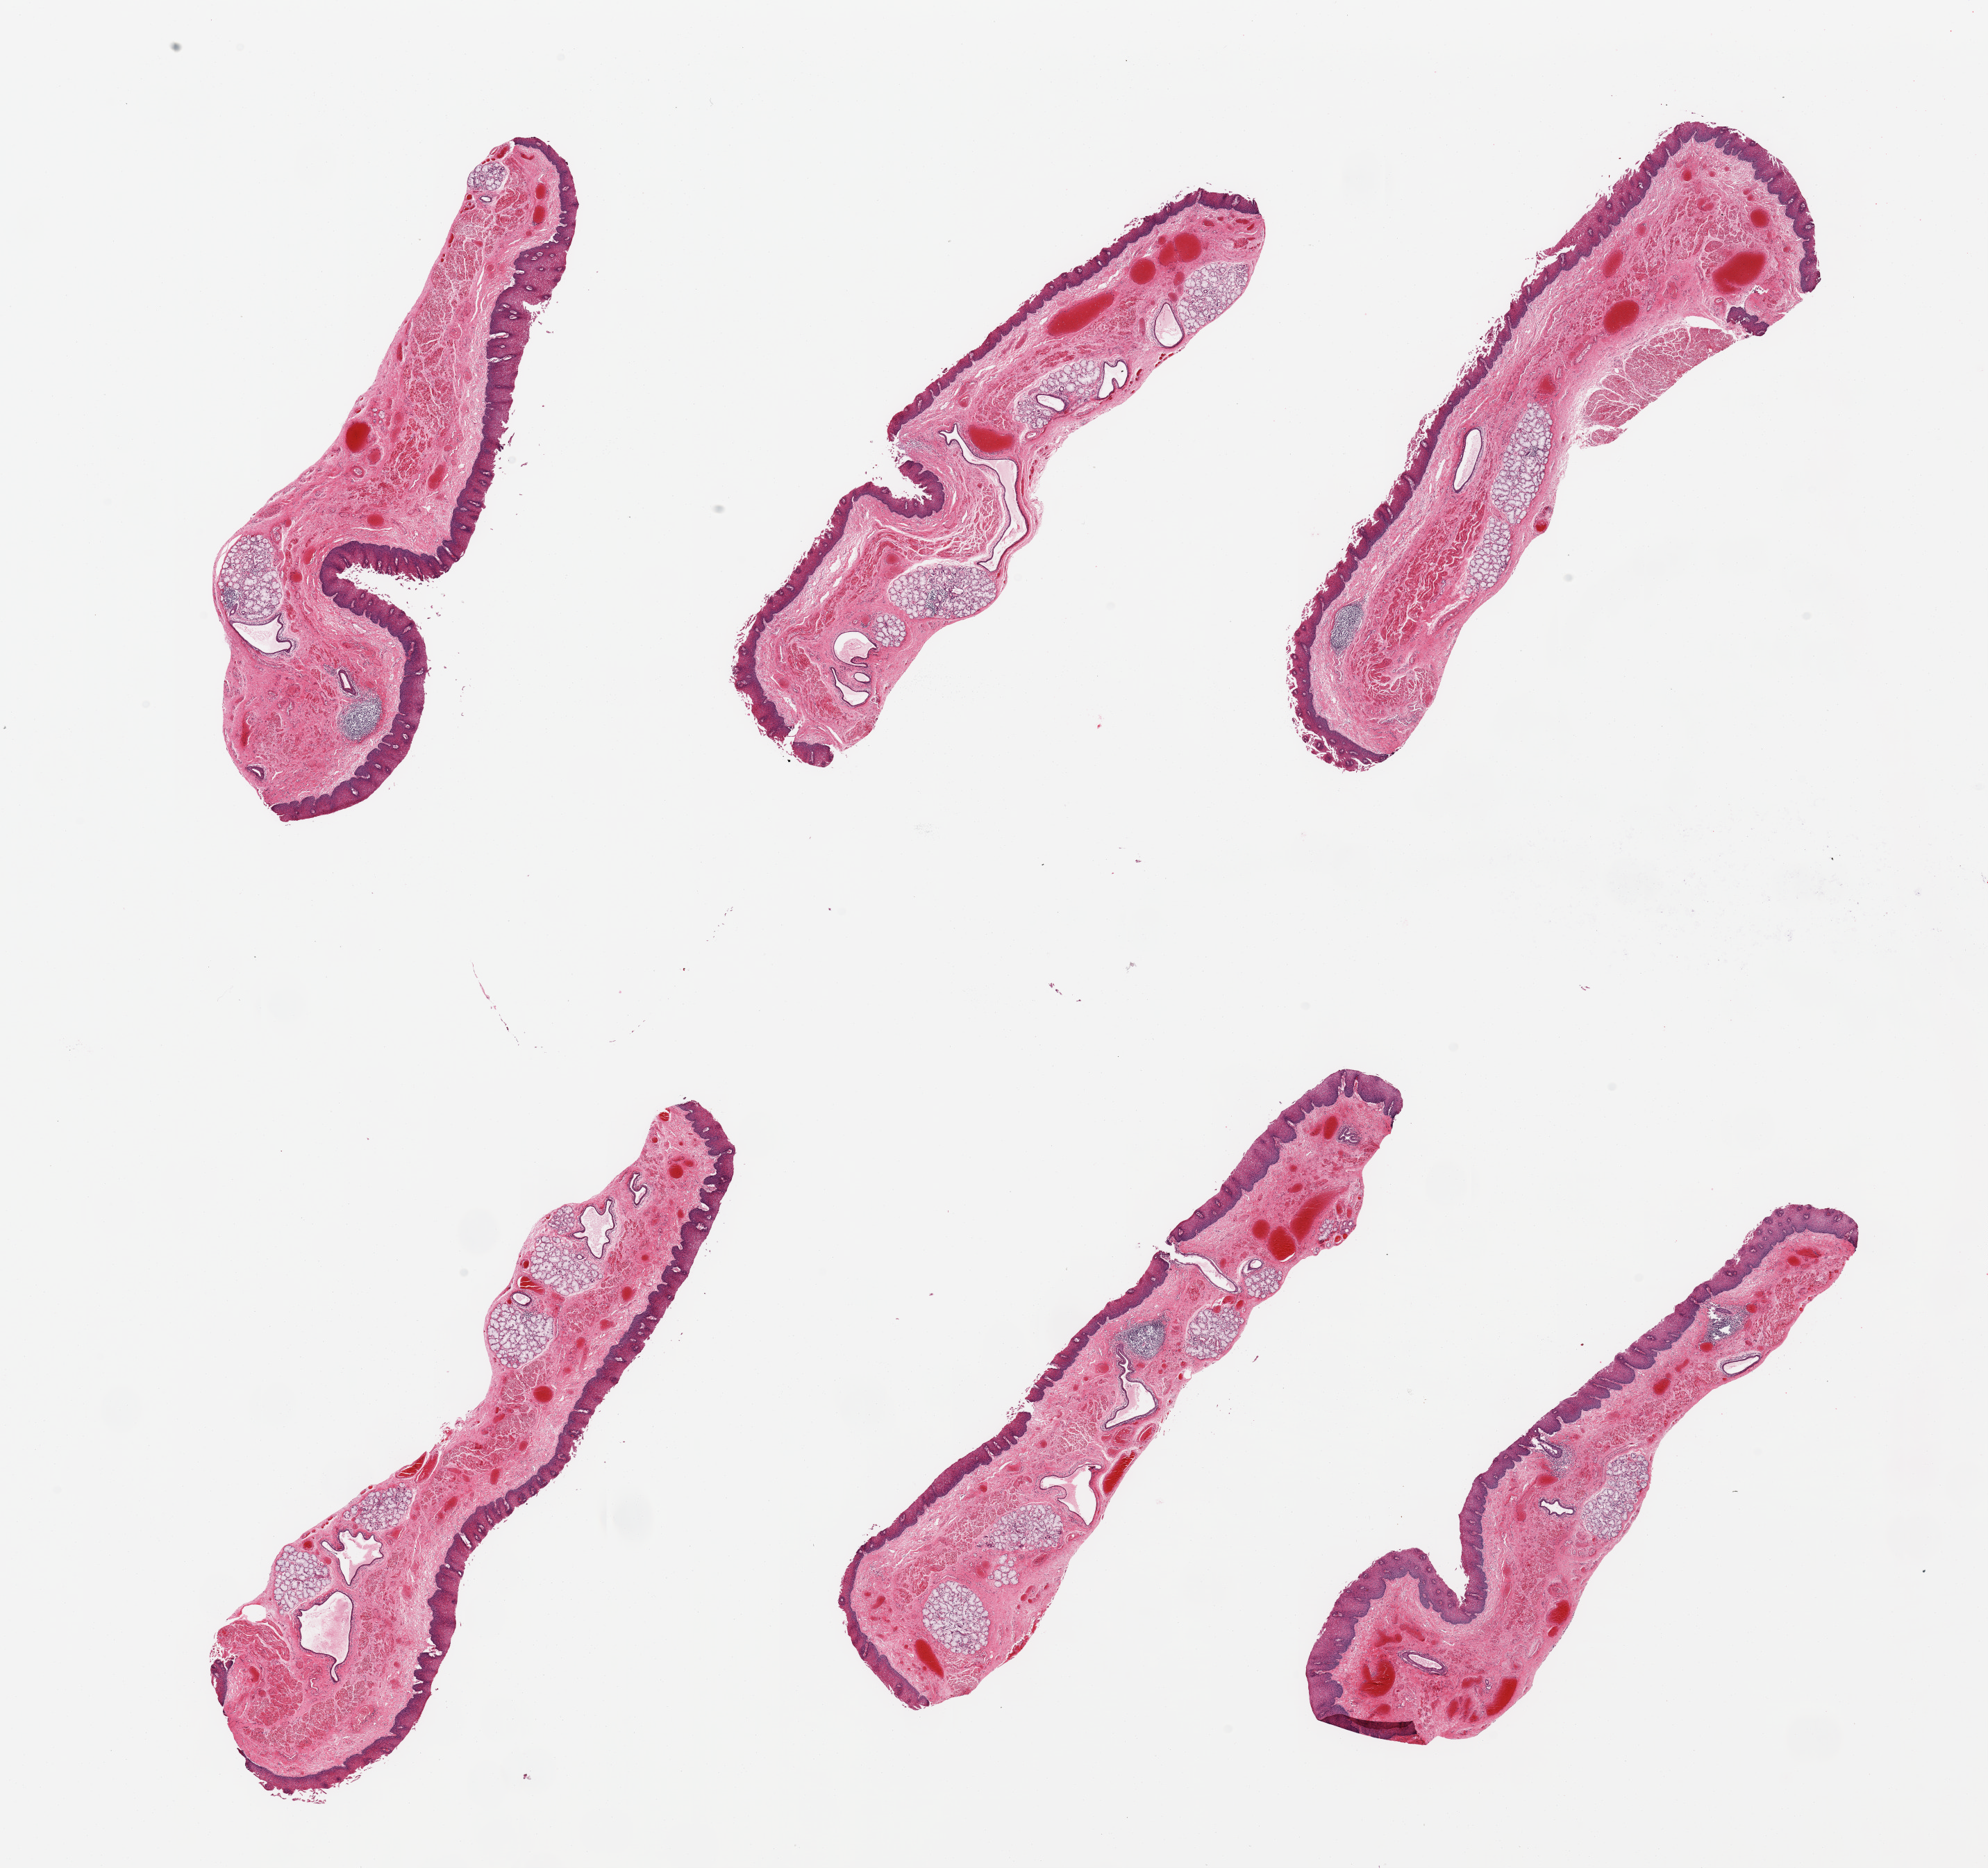
Hematoxylin and eosin (H&E) whole-slide image — shown as a low-resolution overview of the whole scanned area (about 22.6 x 21.3 mm, slide scanned at 20x). PAXgene-fixed, paraffin-embedded tissue. Section of esophageal mucous membrane (target tissue). Donor tissue sample. Male donor.
Pathologist's review note for this sample: 6 pieces, squamous mucosa up to ~0.35mm, ~15-20% thickness; prominent submucosal mucus glands present.